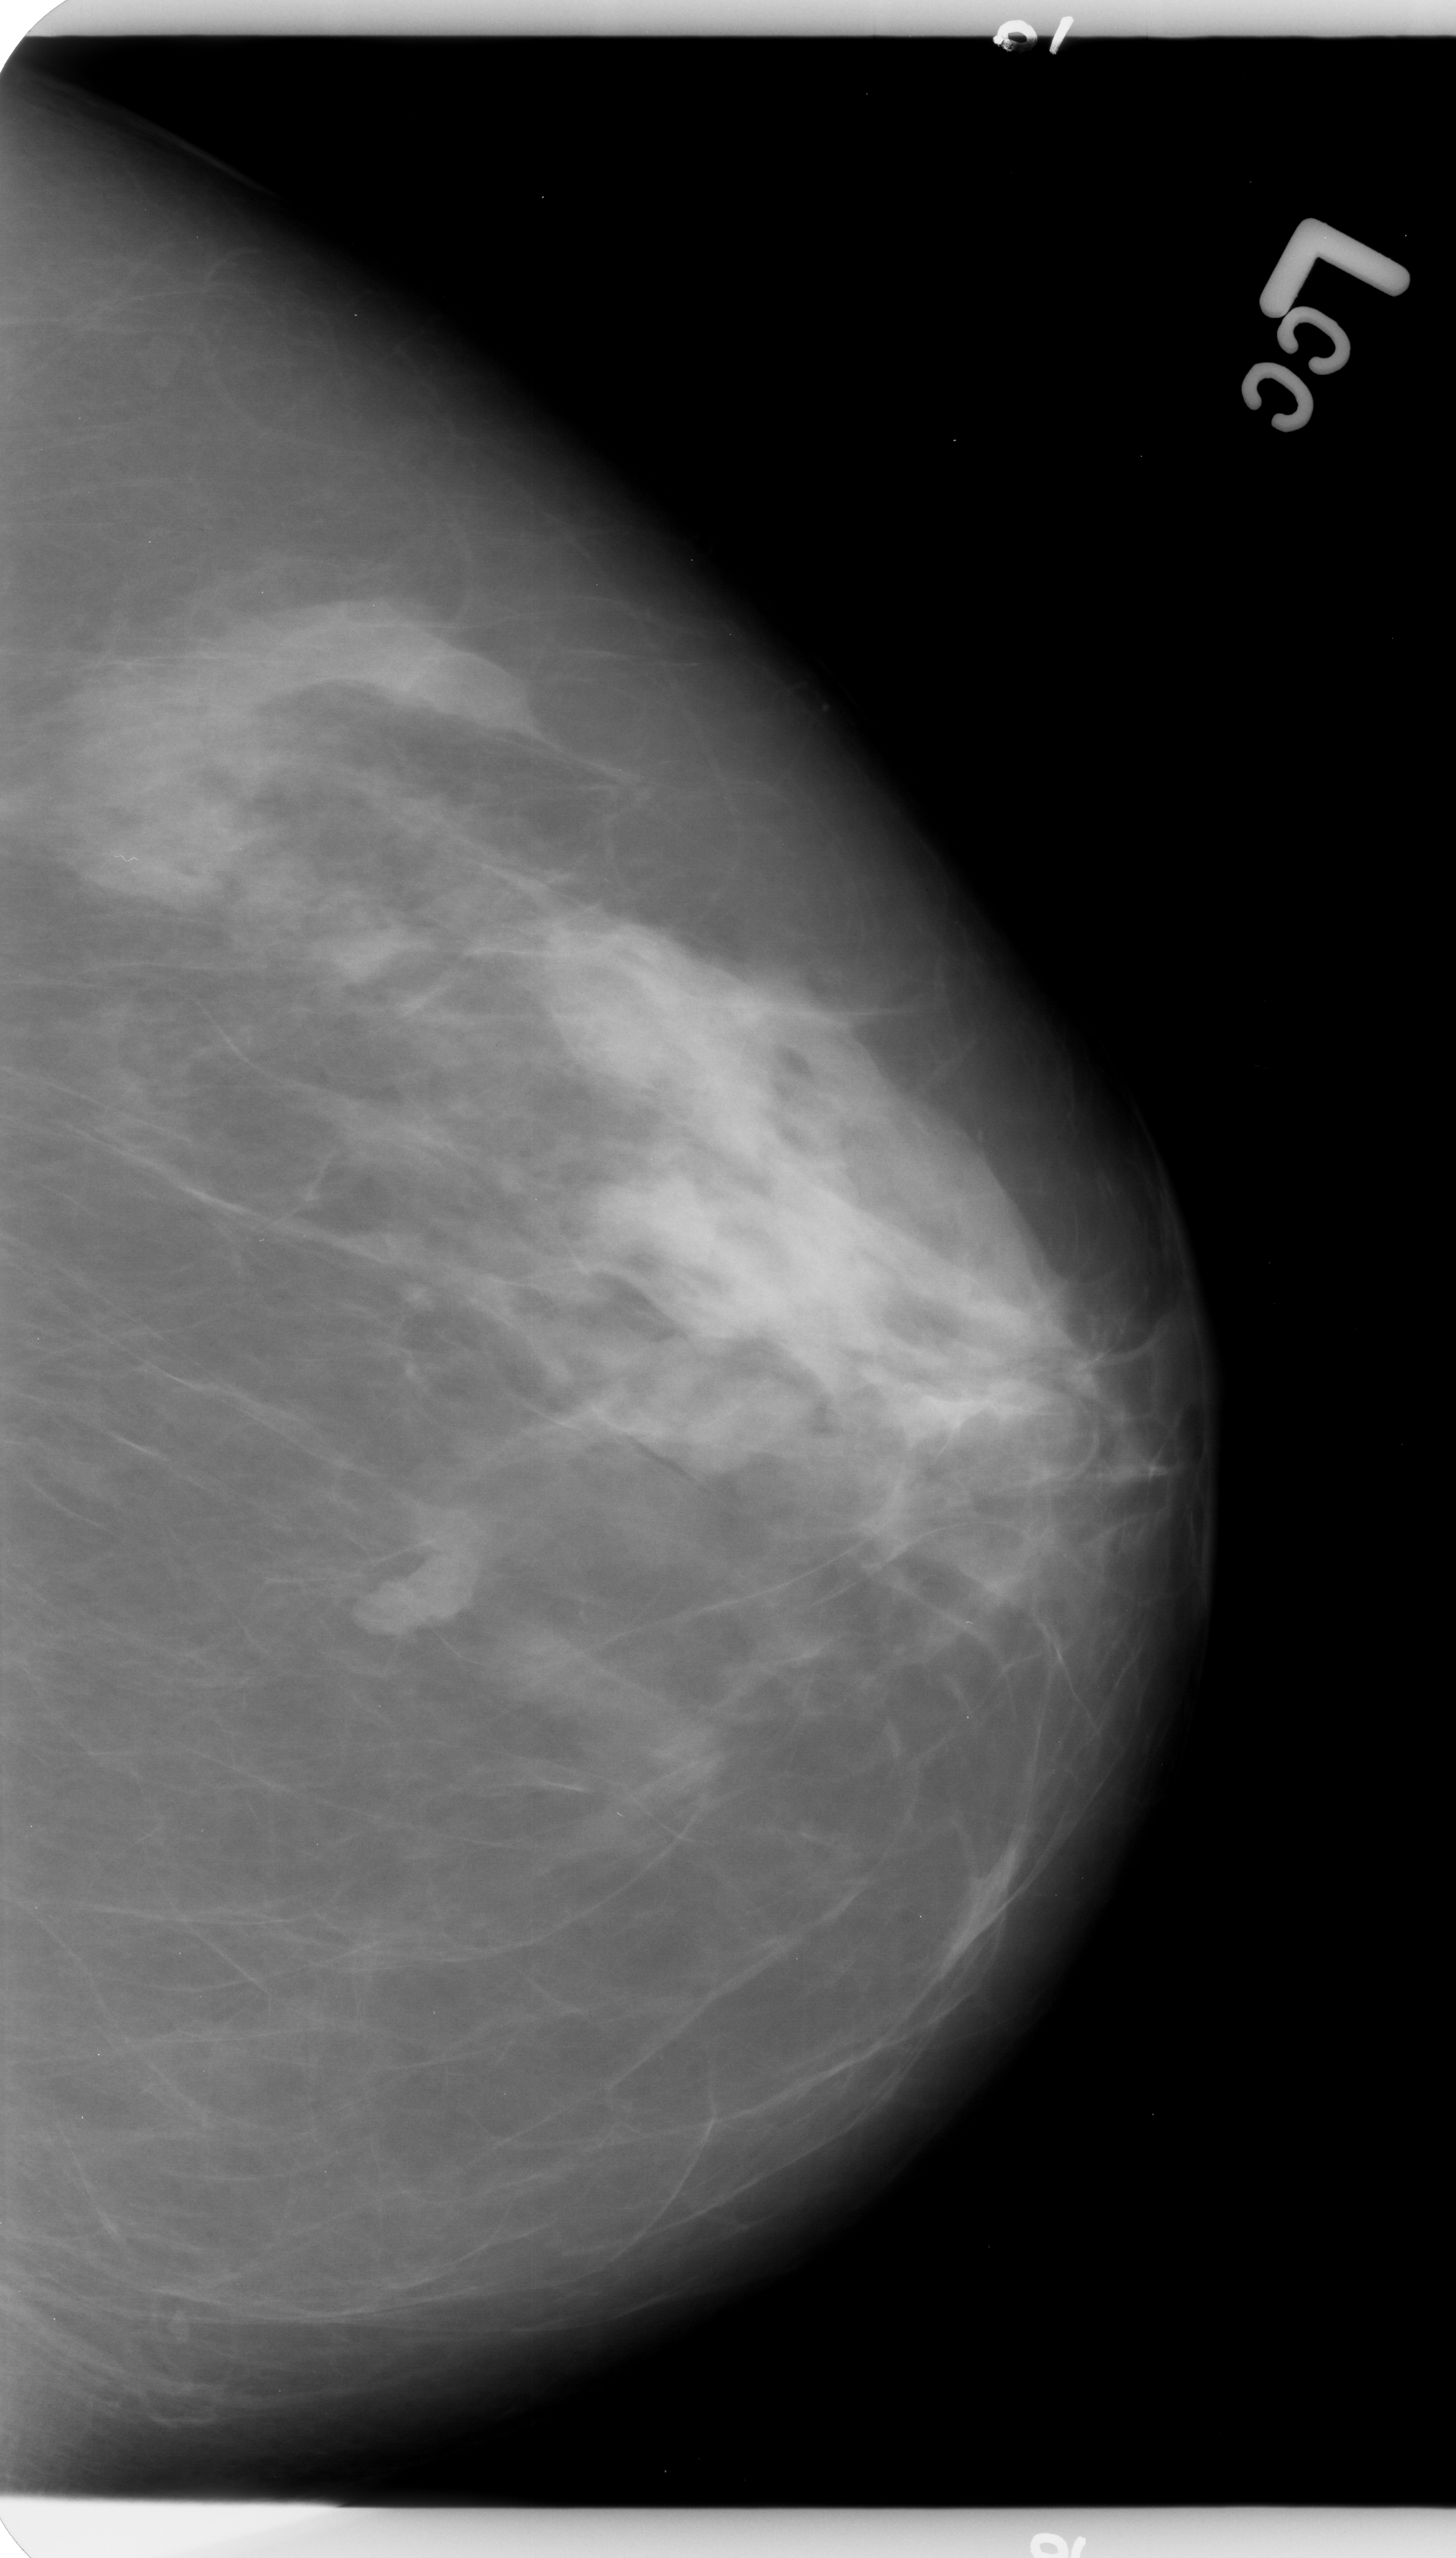
Mammogram (digitized film); left breast; craniocaudal (CC) view; breast composition: scattered fibroglandular densities (BI-RADS density category 2 of 4); 1456 × 2558 image matrix.
Marked abnormalities (boxes around the expert regions of interest):
- mass, shape lobulated, margins circumscribed / microlobulated; BI-RADS assessment category 4; subtlety rating 4 on a 1 (subtle) to 5 (obvious) scale; pathology (as recorded): benign: bounding box <365,1497,492,1636> (left, top, right, bottom; pixels)